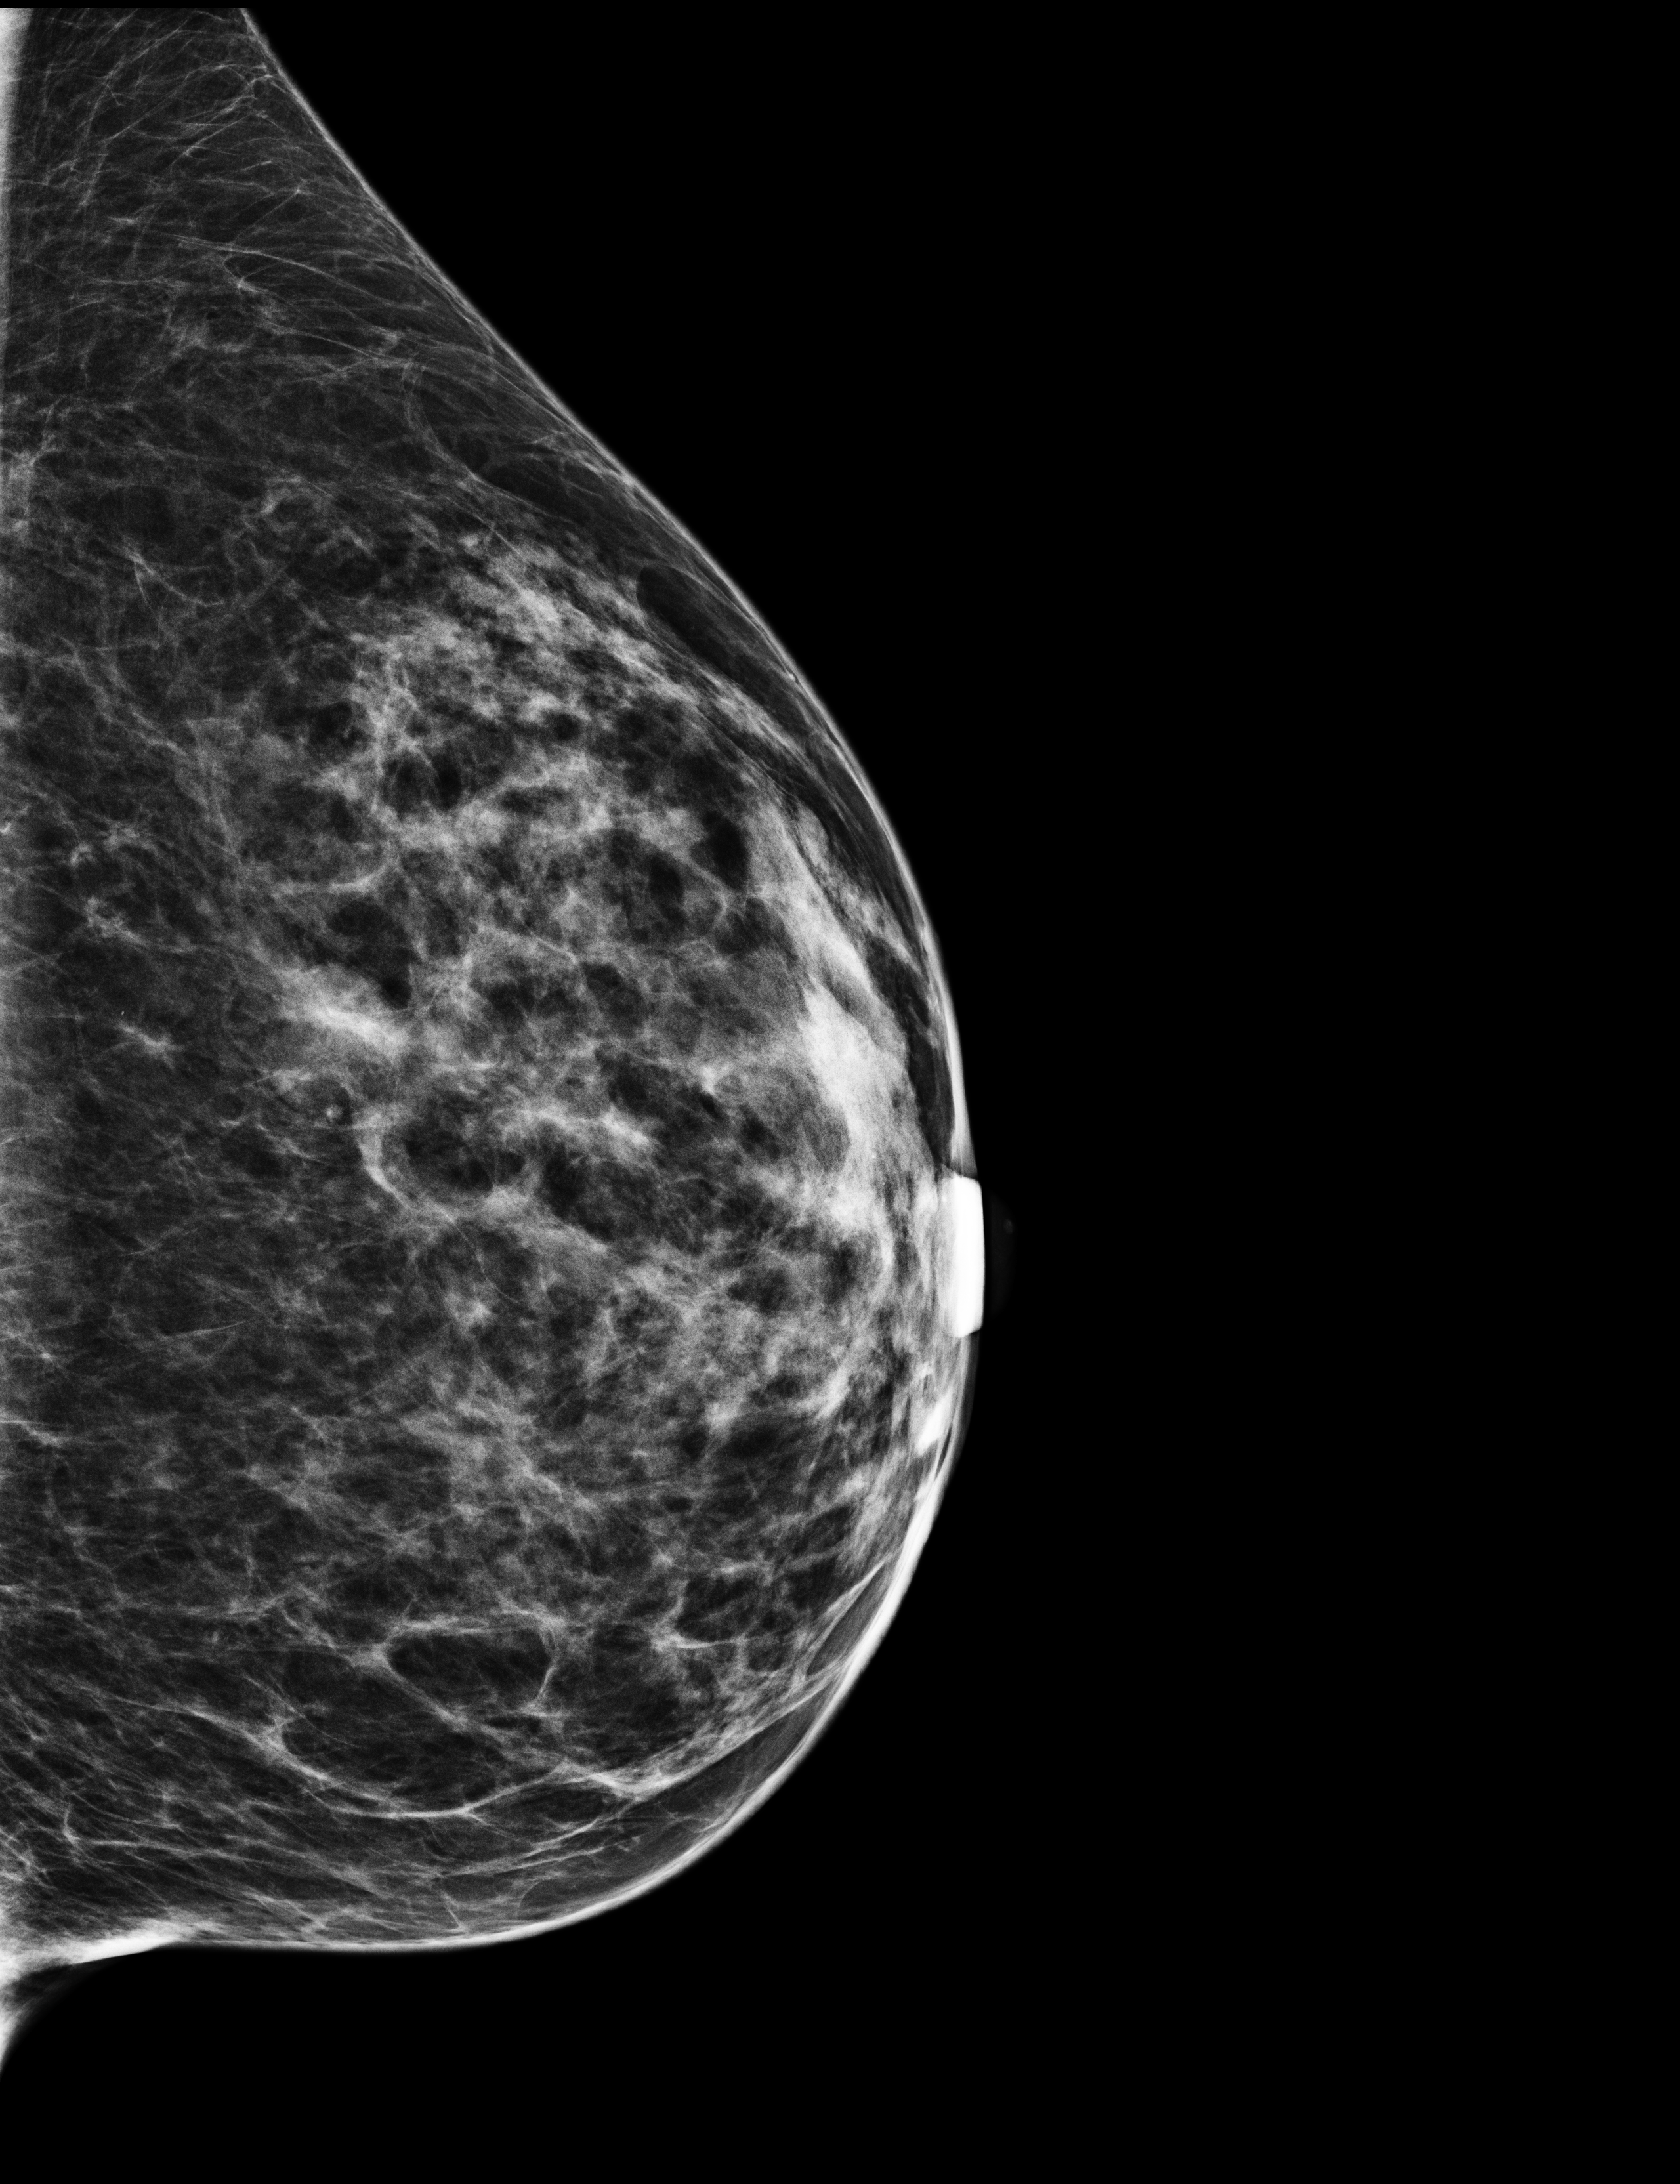
Digital mammogram (FFDM); left breast; LM view; annual screening mammography examination; system: Selenia Dimensions. Patient aged 50 years (female).
- breast density at the screening exam (both breasts): heterogeneously dense (BI-RADS density category c)
- final BI-RADS assessment for this screening round (tomosynthesis exam, both breasts): category 1
- recall: no recall after this screen